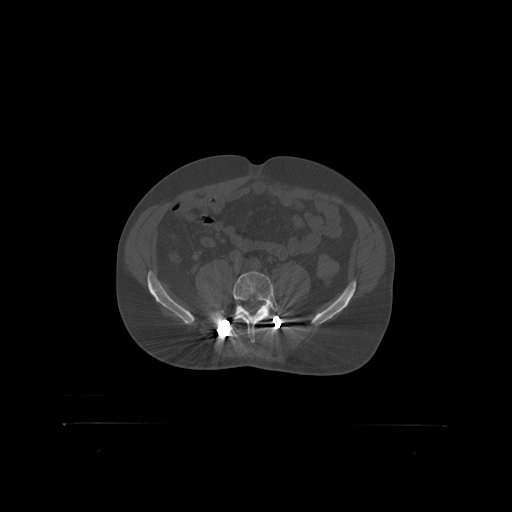
CT including the spine, one axial slice. Position 206 of 399 along the scan axis. Reconstruction kernel STANDARD. Bone window (W 1800 / L 400 HU). 512 × 512 image matrix, field of view 650 × 650 mm. Male patient, age 46 years. From the clinical record (not read from this slice): primary cancer: skin.
Outlined on this slice (semi-automatically segmented with operator editing):
- L5 vertebra: box from (x=233, y=272) to (x=280, y=319) px